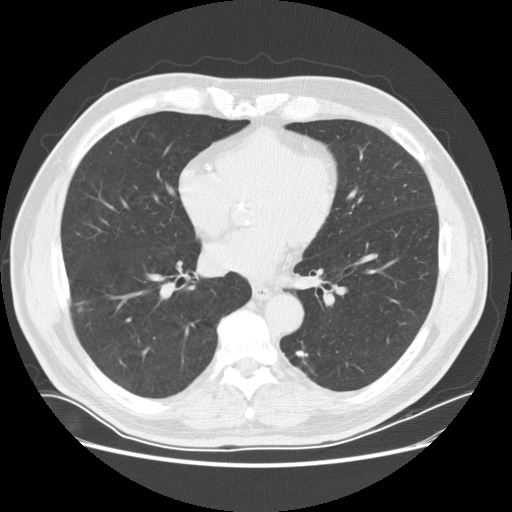
Axial slice from a low-dose chest CT screening exam; baseline annual screen; lung window (W 1500 / L -600 HU); 2.5 mm slice thickness; 512 × 512 image matrix. Male participant, aged 72 years at enrolment. Current smoker at enrolment.
Expert reader's lesion annotation, bounding box [x1, y1, x2, y2] px = [63, 293, 95, 326]. Reader record for this screening exam (exam-level; its link to the box is not recorded): non-calcified nodule or mass ≥4 mm, right lower lobe, 13 × 8 mm, poorly defined margins, soft tissue attenuation. Participant outcome: lung cancer diagnosed 17 days after this screen — non-small cell carcinoma, right lower lobe, moderately differentiated (G2), stage IA (AJCC 6th edition), 10 mm at pathology.